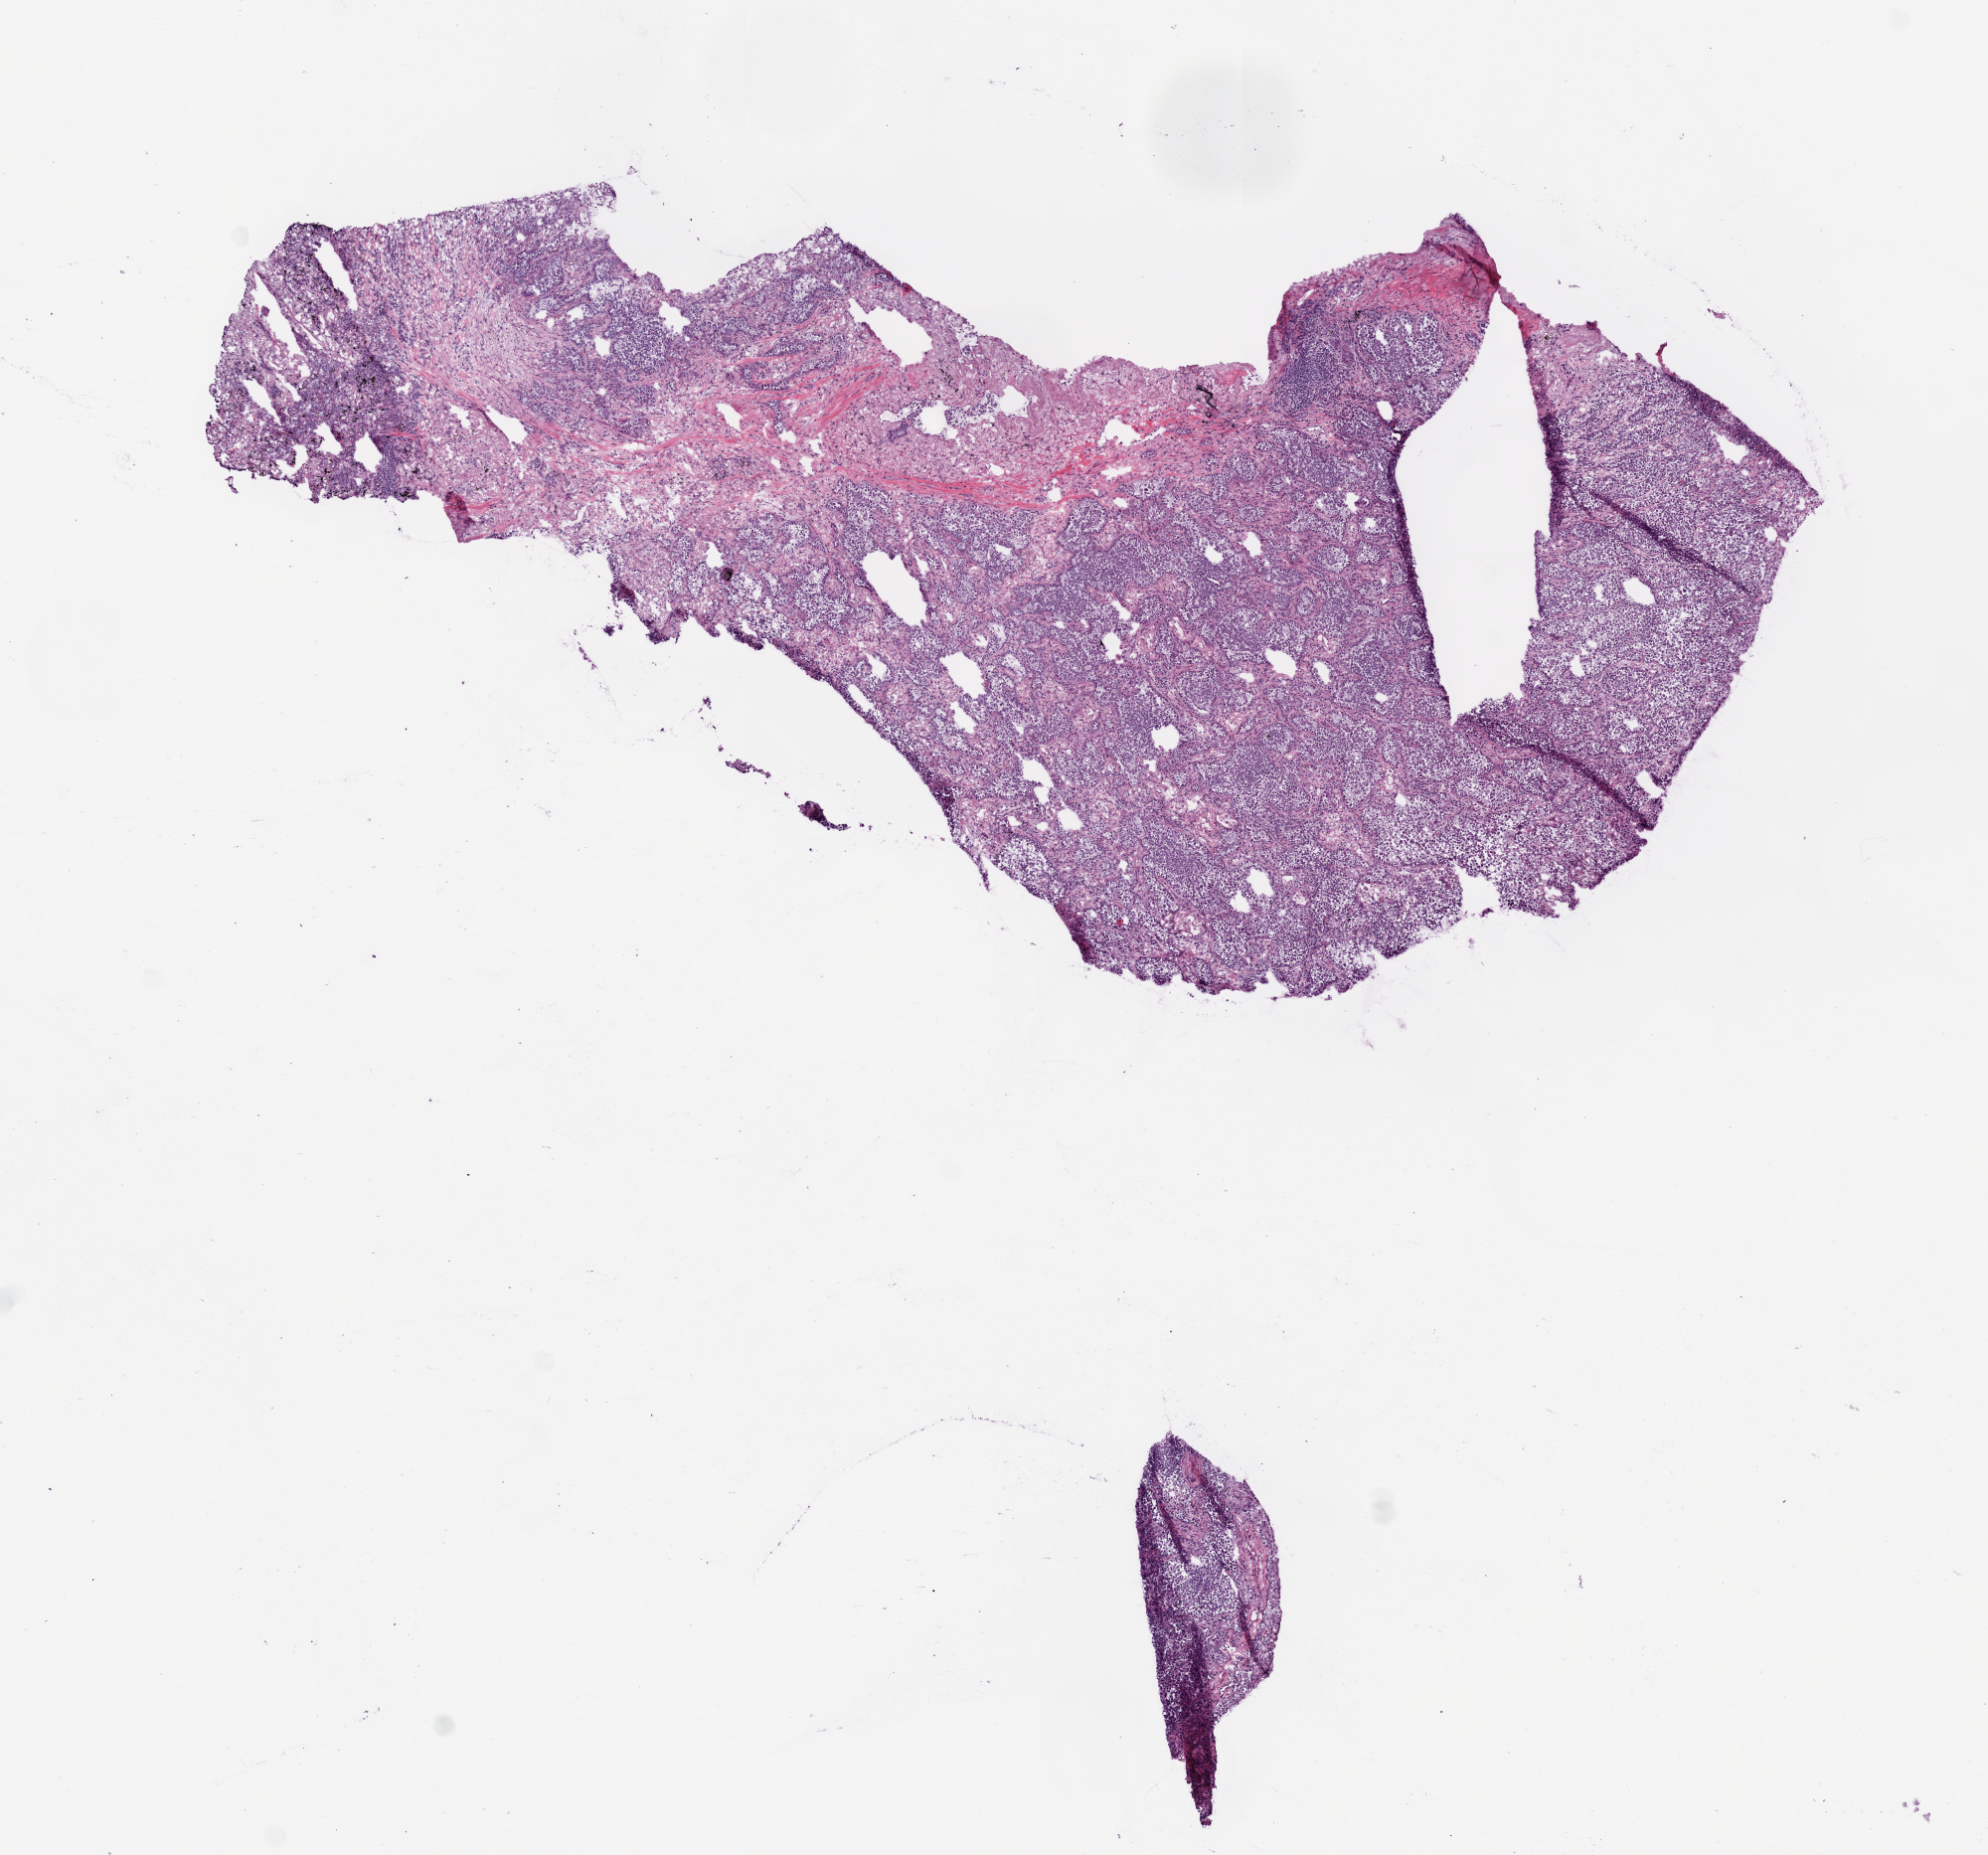
Whole-slide histology image, H&E-stained — a low-resolution overview of the entire scanned area, about 8.0 x 7.5 mm (from a 20x scan), frozen section, primary tumour sample from the lung. Female patient; age at initial diagnosis 84 years. Composition of this section per pathologist review: tumour cells 85%, tumour nuclei 80%, normal cells 0%, stromal cells 15%, necrosis 0%.
- TNM: T2 N0 M0
- histologic diagnosis: Adenocarcinoma, NOS (lower lobe, lung)
- AJCC pathologic stage: IB
- laterality: left